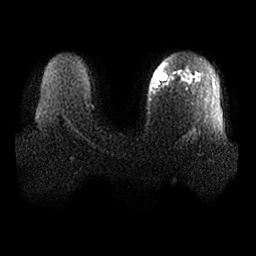
Breast MRI, one axial slice; position 21 of 25 along the scan axis; diffusion-weighted series; image 2 of 4 stored at this slice position (different b-values; order by instance number); 1.5 T; 256 × 256 image matrix, field of view 380 × 380 mm. Female patient.
Annotated regions visible in this slice (manually delineated by an expert):
- tumour on diffusion-weighted imaging: box from (x=158, y=74) to (x=168, y=82) px